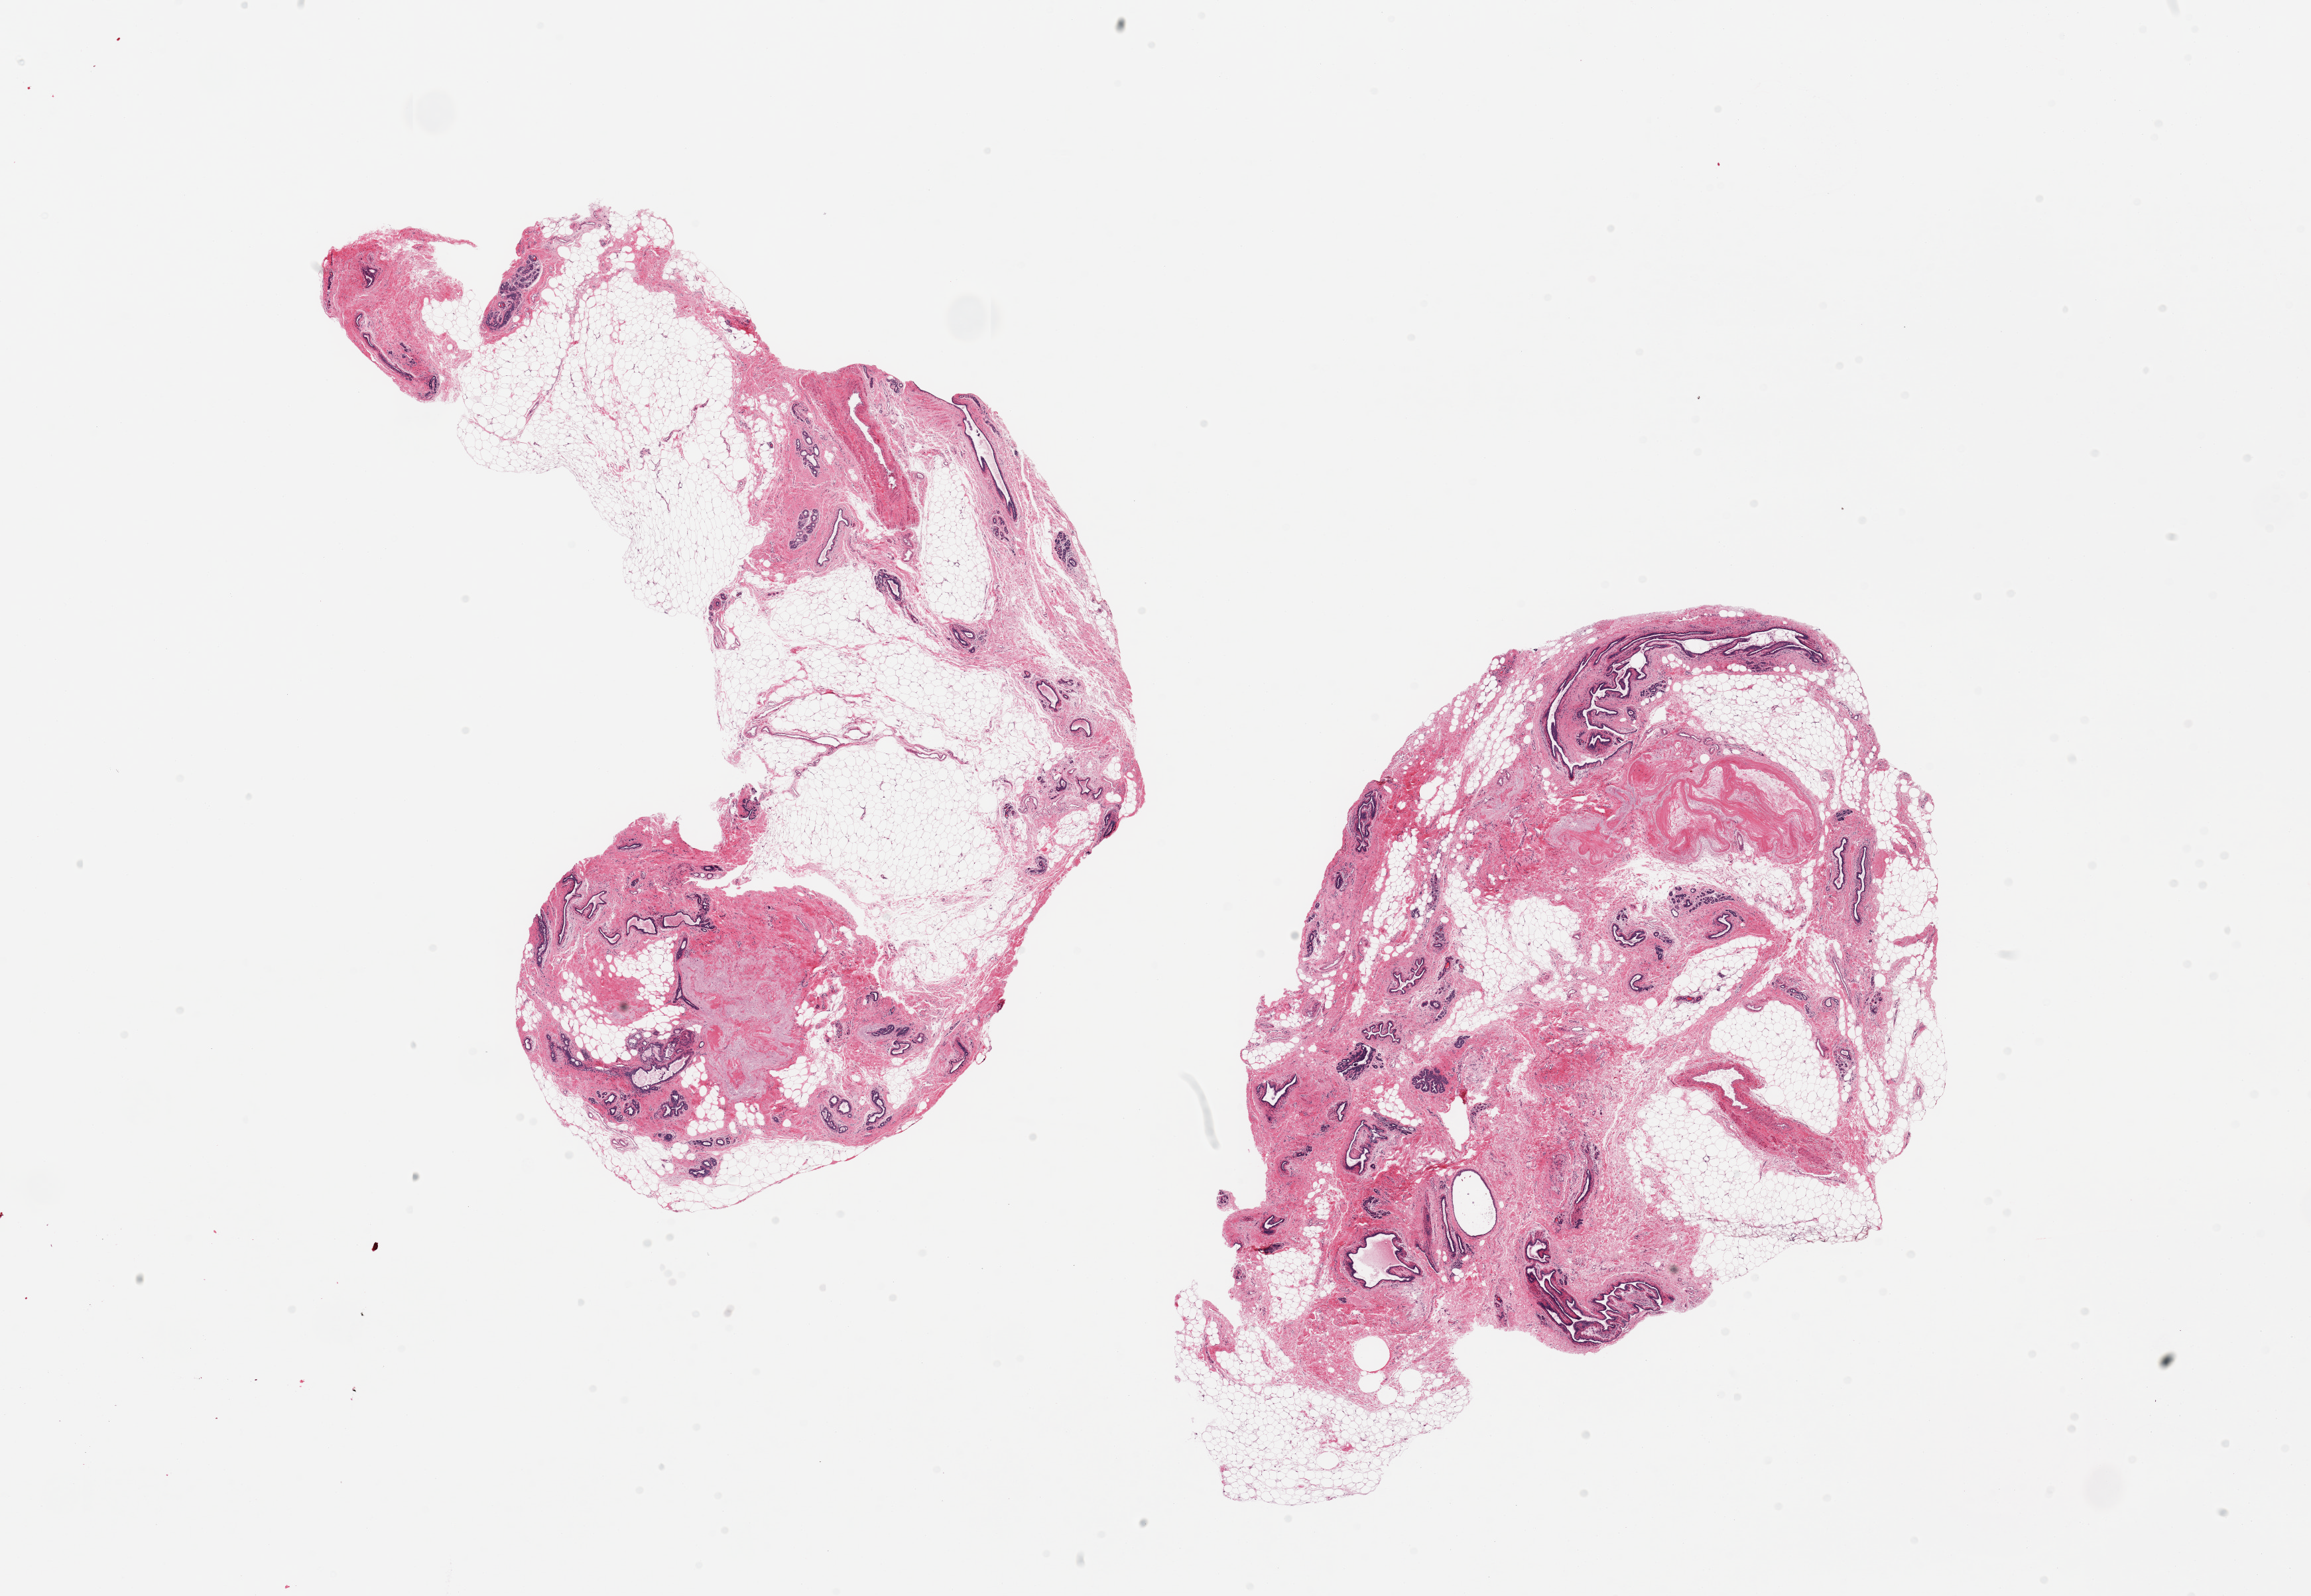
Digitized H&E-stained section, brightfield — a low-resolution overview of the entire scanned area, about 27.6 x 19.0 mm. PAXgene-fixed paraffin-embedded (PFPE) section. Sampled site (target tissue): breast. Donor tissue sample.
Pathologist's review note for this sample: 2 pieces; atrophic ductal & lobular units; 40 & 60% fat content.